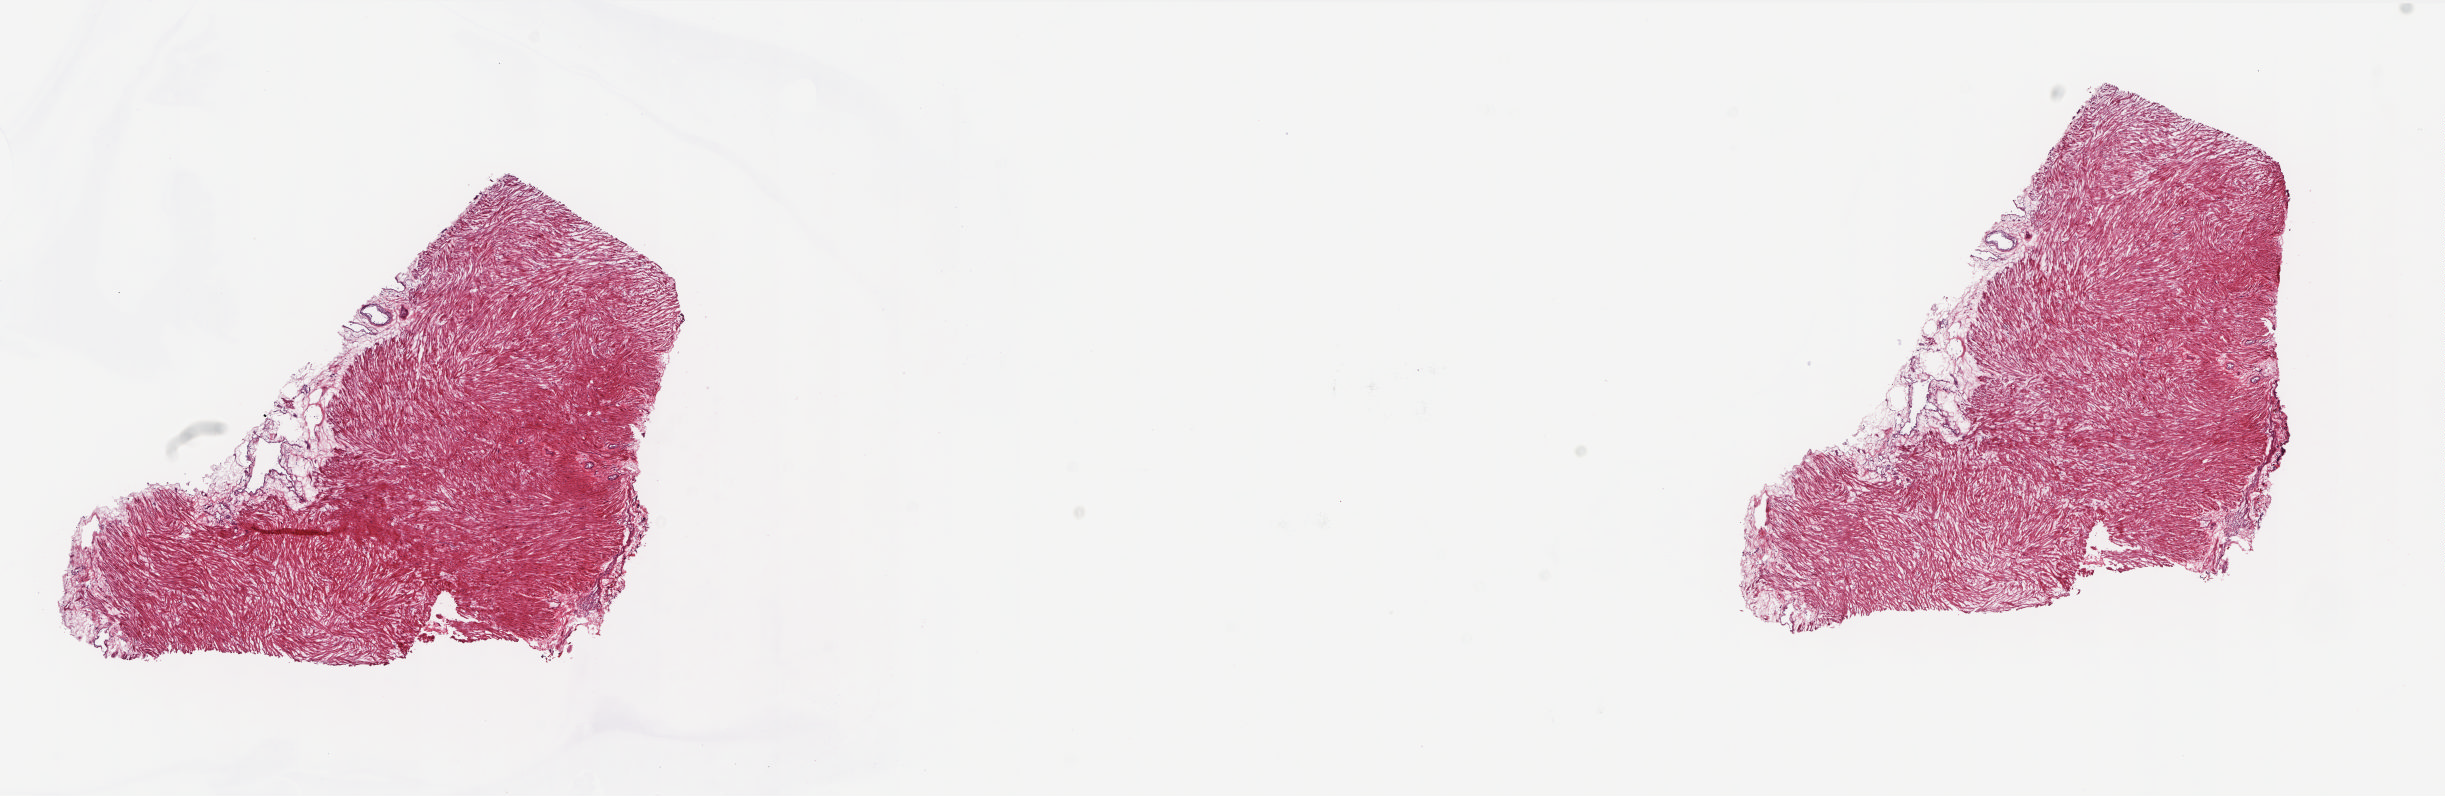
Whole-slide histology image, H&E-stained — whole scanned area (about 19.7 x 6.4 mm, from a 20x scan) shown as a low-resolution overview, frozen section from the top of the tissue portion, sample: solid tissue normal (non-tumour tissue), prostate. Male, age 68 years at initial diagnosis. Slide review estimates, as recorded: tumour cells 0%, tumour nuclei 0%, normal cells 100%, stromal cells 0%, necrosis 0%. Inflammatory infiltration, as recorded: lymphocyte infiltration 1%, monocyte infiltration 0%, neutrophil infiltration 0%.
• this section: solid tissue normal (non-tumour) sample from the same patient
• patient diagnosis: Adenocarcinoma, NOS (prostate gland)